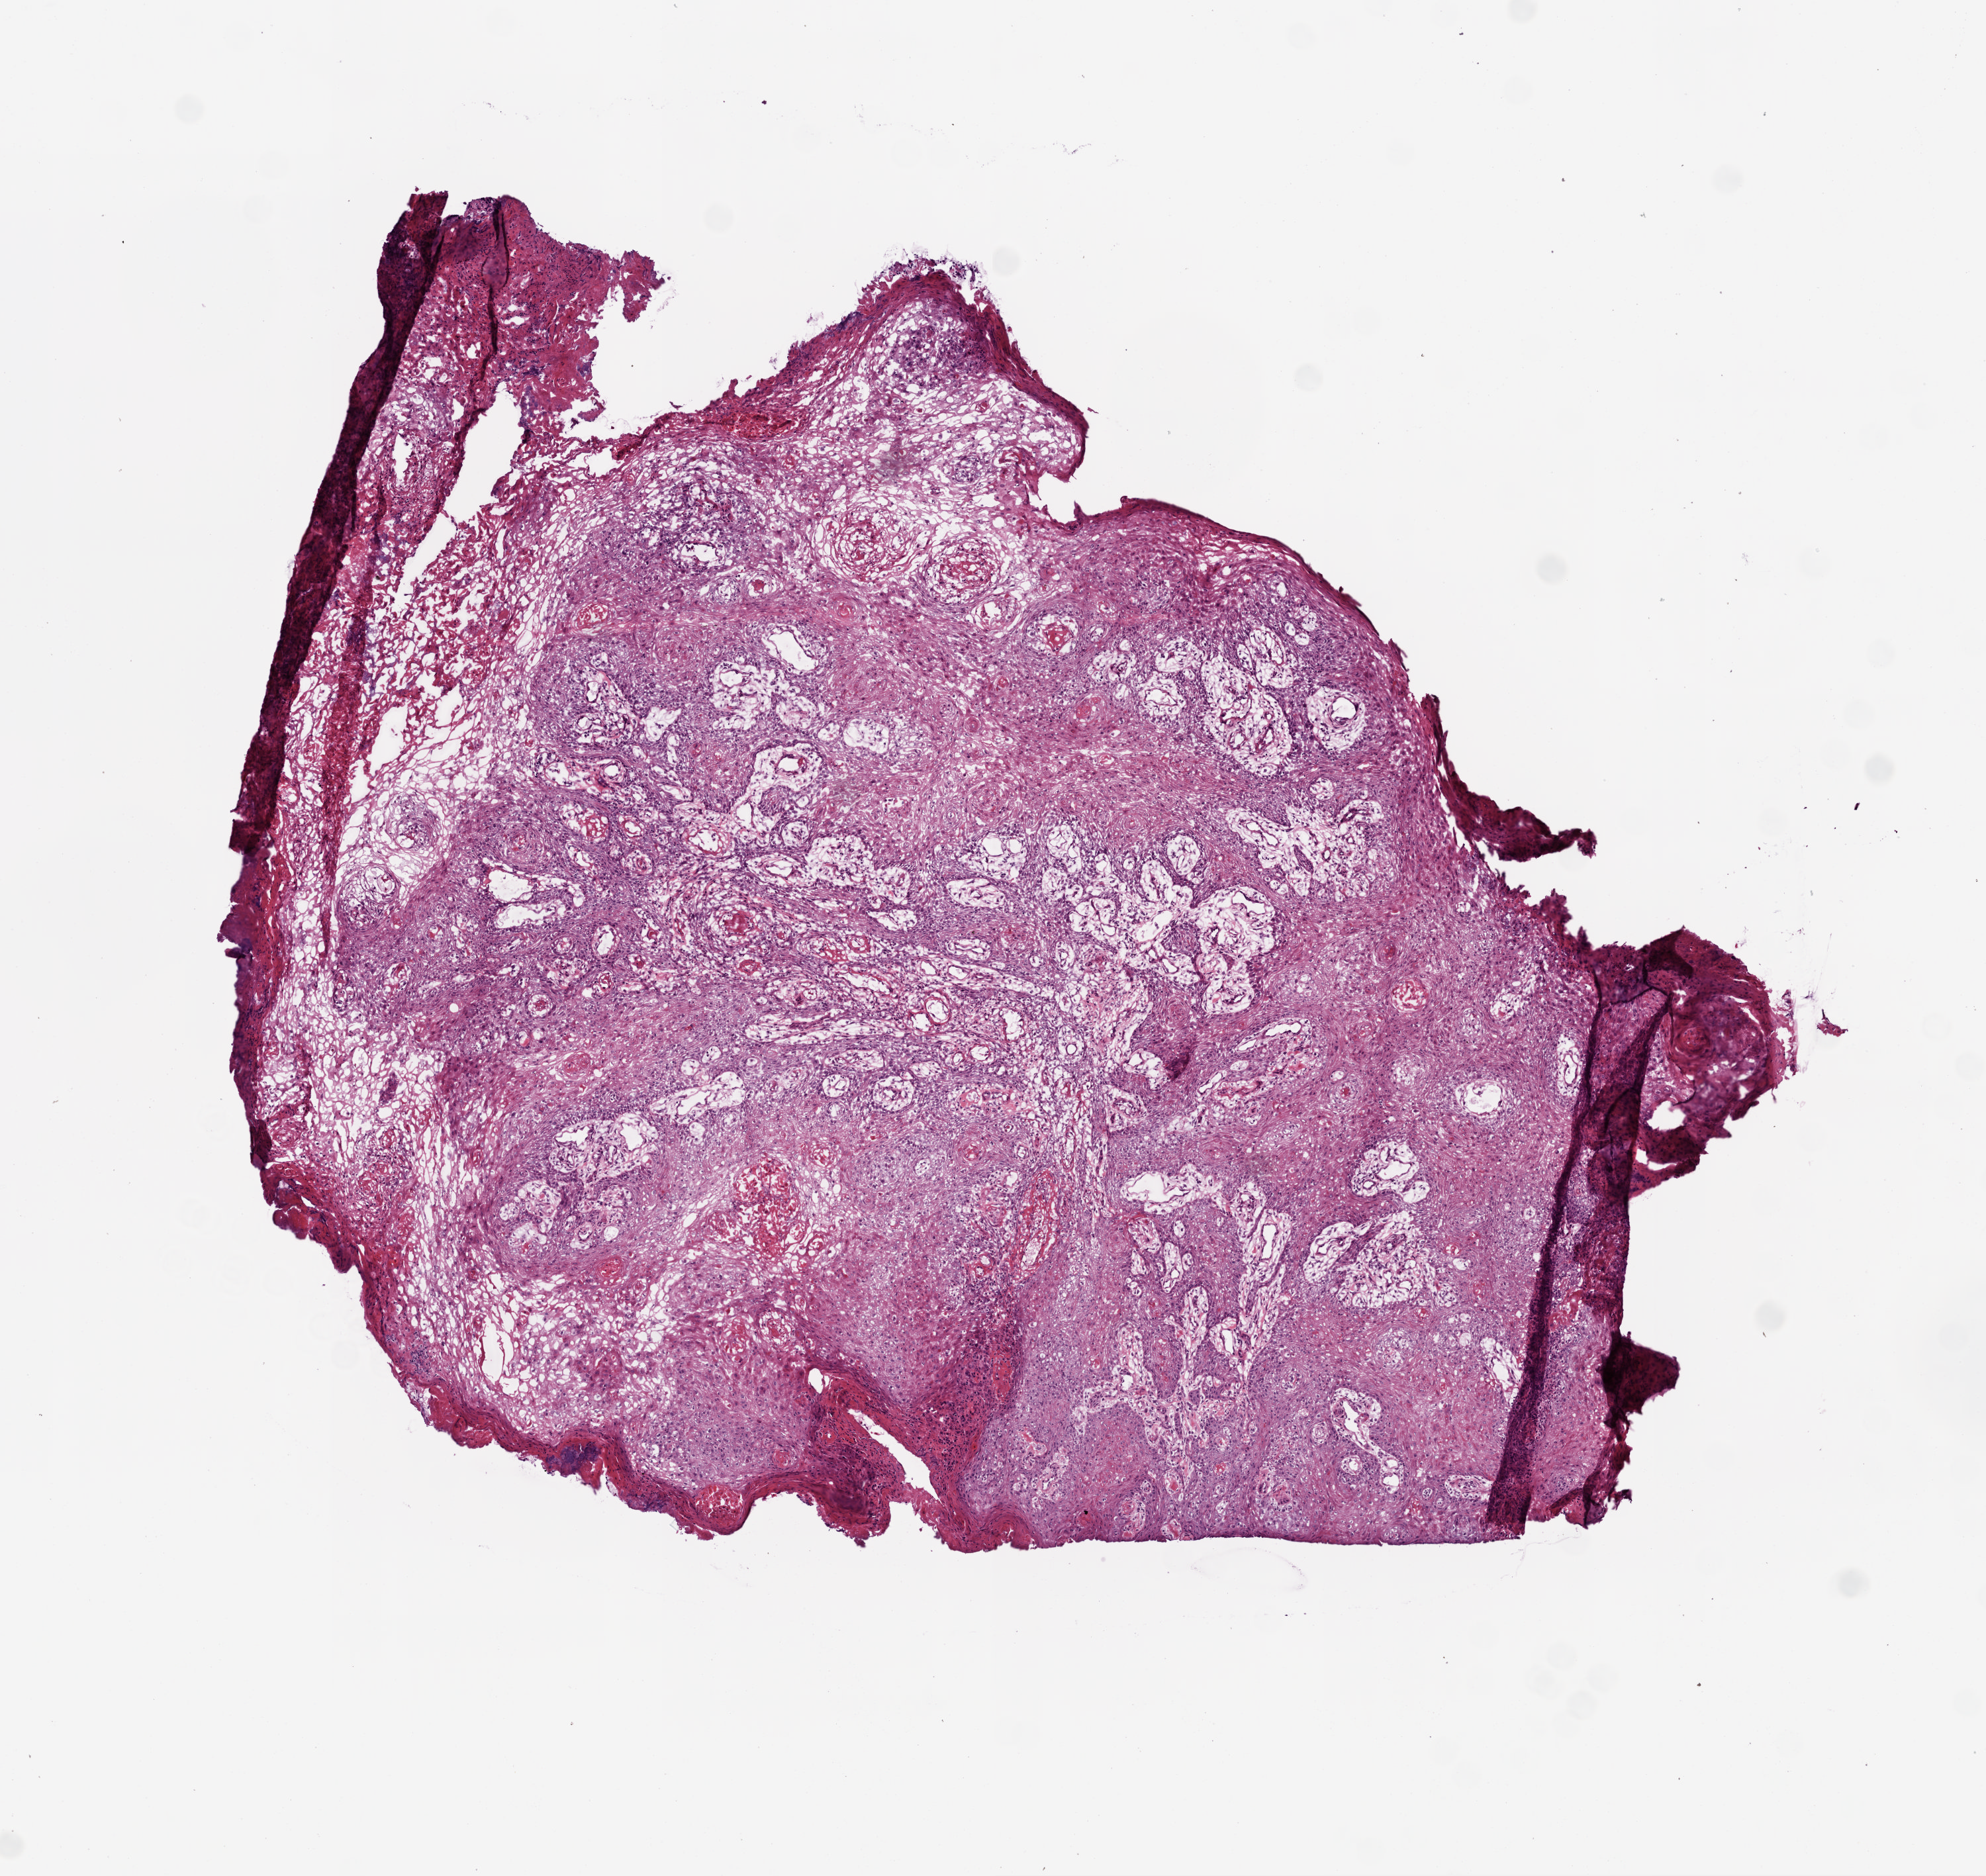
Hematoxylin and eosin (H&E) stained whole-slide image, shown as a low-resolution overview of the whole scanned area (about 6.0 x 5.7 mm); frozen section from the top of the tissue portion; sample: primary tumour, head and neck. Male, age 70 years at initial diagnosis. Histologic grade: G2 (moderately differentiated). Composition of this section per pathologist review: tumour cells 90%, tumour nuclei 85%, normal cells 0%, stromal cells 10%, necrosis 0%.
AJCC pathologic stage: II (7th edition). Diagnosis: Squamous cell carcinoma, NOS (cheek mucosa).